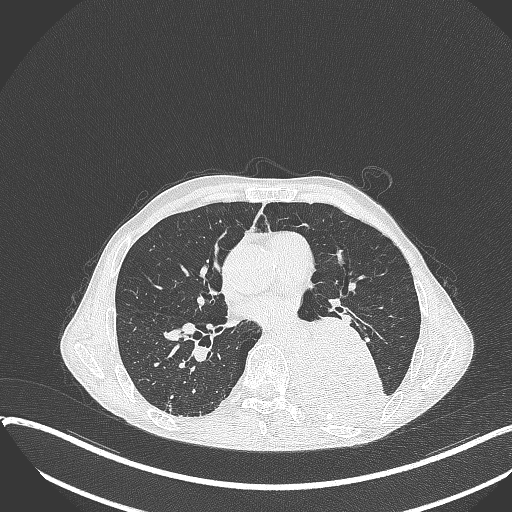
Chest CT, one axial slice. 120 kVp. Lung window (W 1500 / L -600 HU). 512 × 512 image matrix, field of view 400 × 400 mm. Male patient, age 57 years. Case-level facts recorded for this patient, not image findings: clinical TNM (as recorded): T4 N0 M0.
Annotated regions visible in this slice (rectangle marked by the reading radiologist):
- lung tumour (recorded histology: squamous cell carcinoma): bounding box (x1, y1, x2, y2) in pixels: (295, 313, 391, 425)